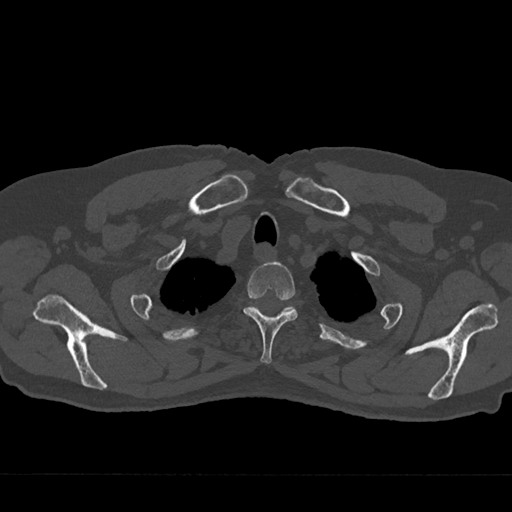
CT including the spine, one axial slice; slice 606 of 797 in the series (ordered by position); 120 kVp; bone window (W 1800 / L 400 HU); 512 × 512 image matrix, field of view 377 × 377 mm. Male patient, age 75 years. From the clinical record (not read from this slice): primary cancer: renal.
Outlined on this slice (semi-automatic segmentation, software-assisted and operator-edited):
- T2 vertebra: bounding box [x1, y1, x2, y2] px = [243, 261, 298, 364]
- T3 vertebra: [254, 306, 294, 312]